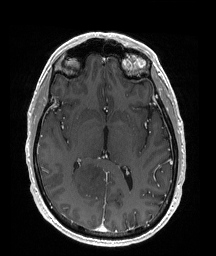
Brain MRI from a brain-tumour surgery series, one axial slice; position 96 of 176 along the scan axis; T1-weighted post-contrast; 216 × 256 image matrix, field of view 211 × 250 mm. From the clinical record (not read from this slice): histopathology: Oligodendroglioma; WHO grade: 2; IDH mutation: yes; tumour location: Right Parietal.
Outlined on this slice (outlined manually by an expert reader):
- tumour: bounding box <70,159,111,196> (left, top, right, bottom; pixels)